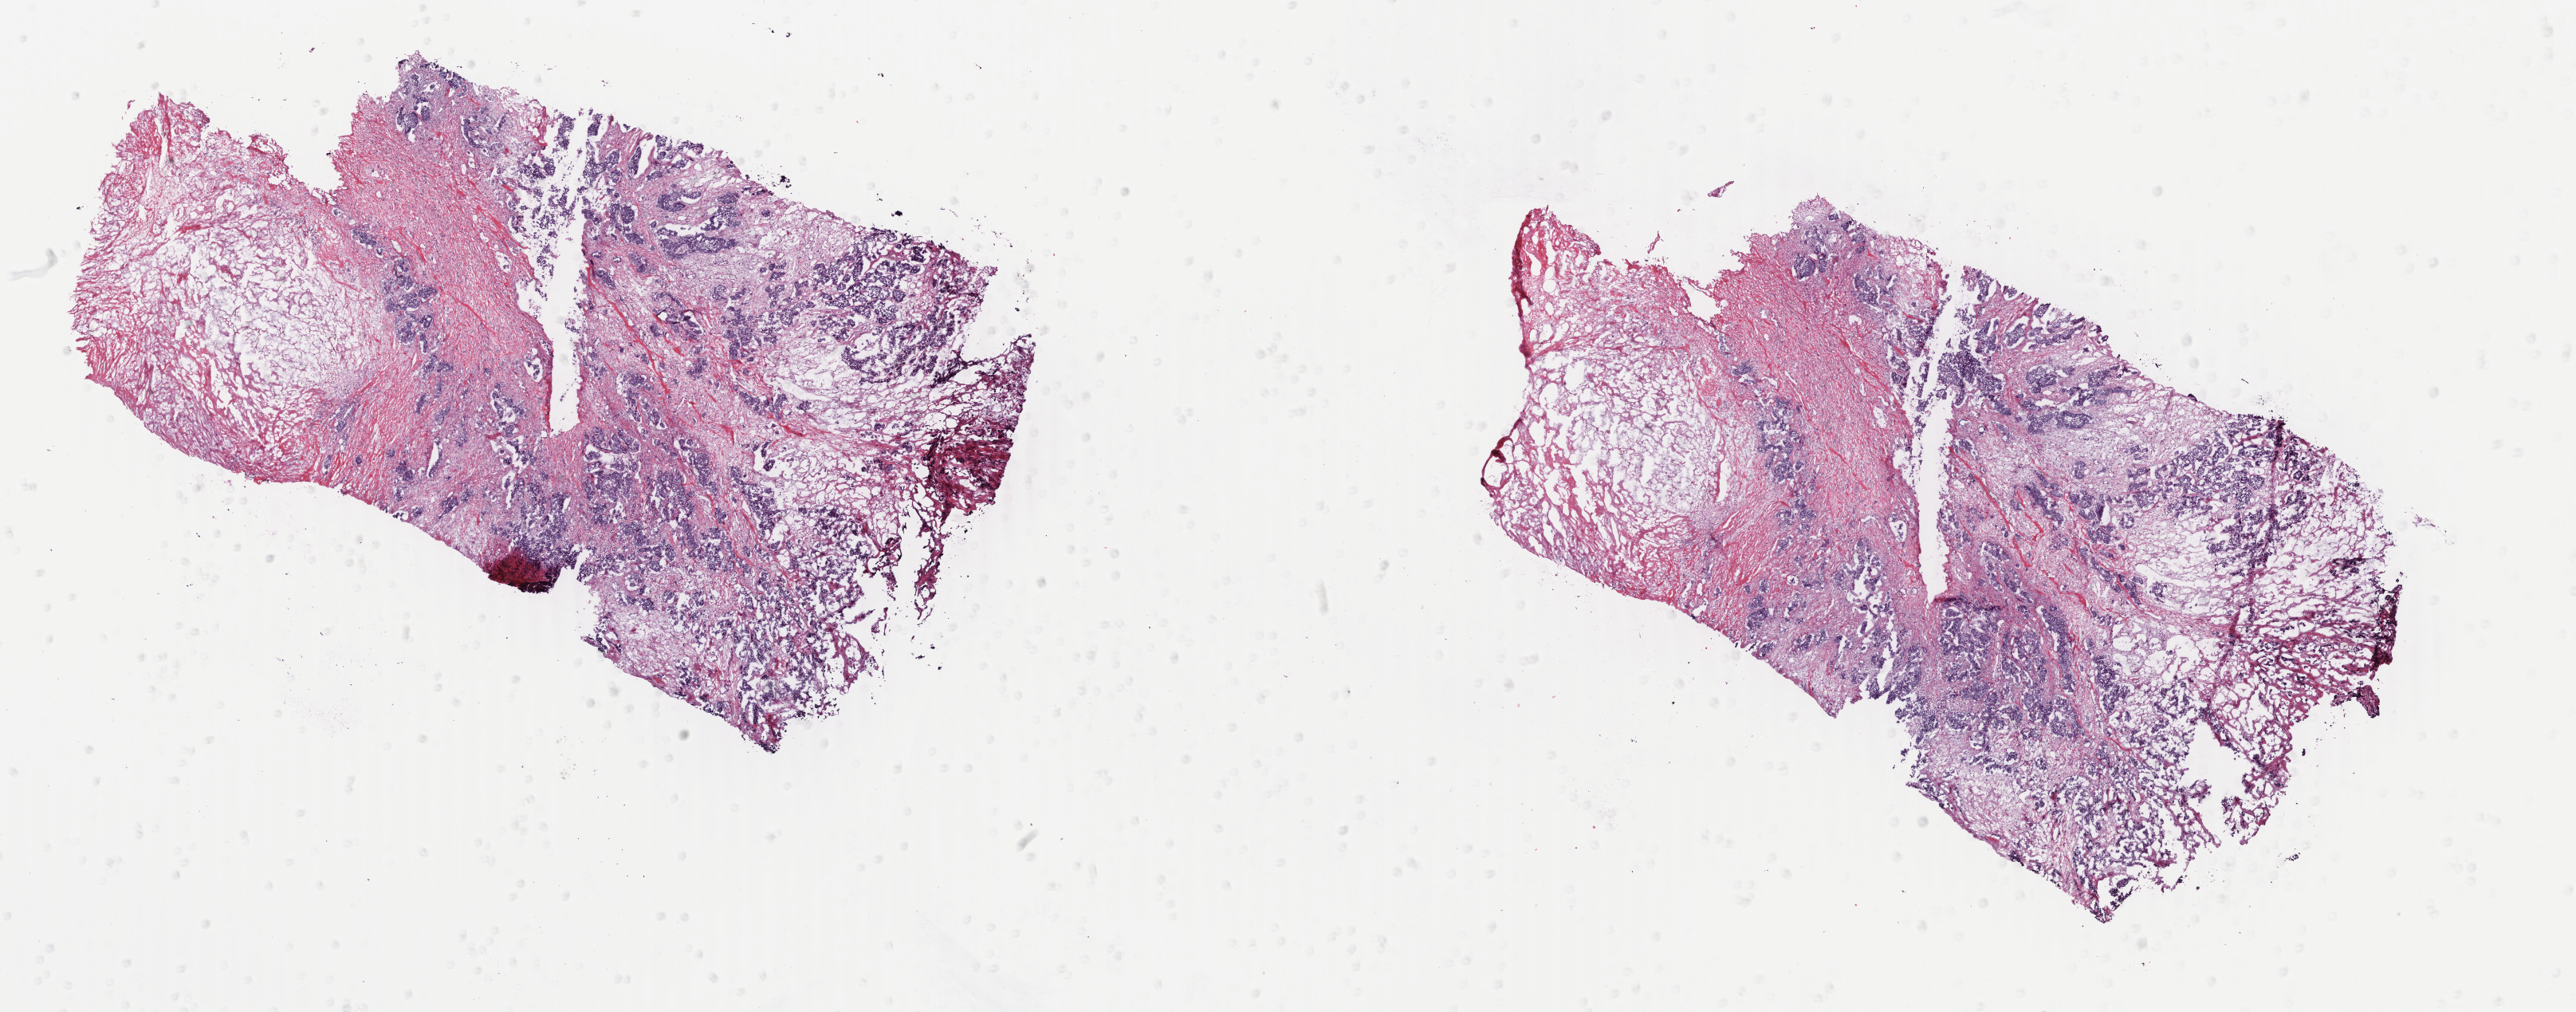
Whole-slide histology image, H&E-stained, shown as a low-resolution overview of the whole scanned area (about 25.7 x 10.1 mm), frozen section, primary tumour sample from the breast. Patient: female, age at initial diagnosis 63 years. Composition of this section per pathologist review: tumour cells 75%, tumour nuclei 85%, normal cells 0%, stromal cells 25%, necrosis 0%. Infiltration values recorded for this section: lymphocyte infiltration 0%, monocyte infiltration 0%, neutrophil infiltration 0%.
AJCC pathologic stage: IIB (6th edition). Diagnosis: Infiltrating duct carcinoma, NOS.